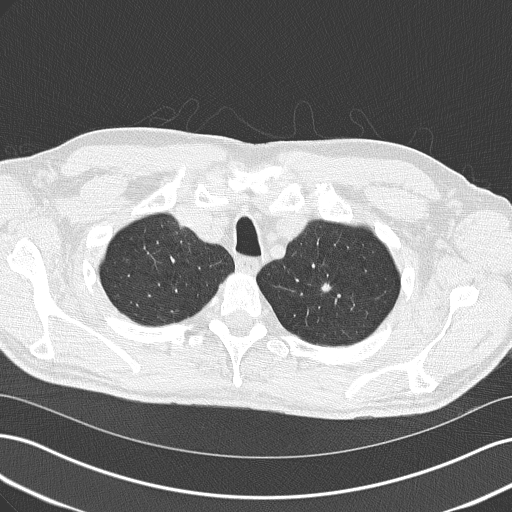
Low-dose screening chest CT, axial slice, second screening round (one year after baseline), lung window (W 1500 / L -600 HU), 2 mm slice thickness, slice 37 of 185 in the series, 512 × 512 image matrix, field of view 360 × 360 mm. Male, age 64 years at enrolment. Former smoker at enrolment.
• Expert reader's lesion annotation, bounding box [x1, y1, x2, y2] px = [301, 272, 340, 309].
• The screening reader recorded 2 non-calcified nodules or masses ≥4 mm on this exam (left upper lobe, left upper lobe); which of them this box marks is not recorded.
• Official screen result: positive, no significant change: stable abnormalities potentially related to lung cancer, unchanged since the prior screening exam.
• Later outcome: lung cancer diagnosed 482 days after this screen — adenocarcinoma, NOS, left upper lobe, poorly differentiated (G3), stage IA (AJCC 6th edition), 10 mm at pathology.